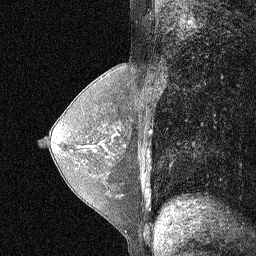
Breast MRI (dynamic contrast-enhanced), one sagittal slice. Position 33 of 64 along the scan axis. Dynamic contrast-enhanced study with each time point stored as its own series, time point 2 of 3 at this slice position (early post-contrast, ordered by acquisition time). 1.5 T. TE 4.5 ms, TR 11 ms. 2.06 mm slice thickness. 256 × 256 image matrix. Female patient, age 55 years. Case-level facts recorded for this patient, not image findings: setting: breast cancer imaged before/during neoadjuvant chemotherapy; receptor status: HR-positive, HER2-negative.
Outlined on this slice (semi-automatically segmented with operator editing):
- analysis volume of interest (the breast-tissue region the enhancement analysis was run in; not a lesion): box from (x=72, y=110) to (x=133, y=190) px
- tumour enhancement mask (voxels above the 90 % enhancement threshold inside the analysis volume of interest): (x=94, y=150)–(x=96, y=152)